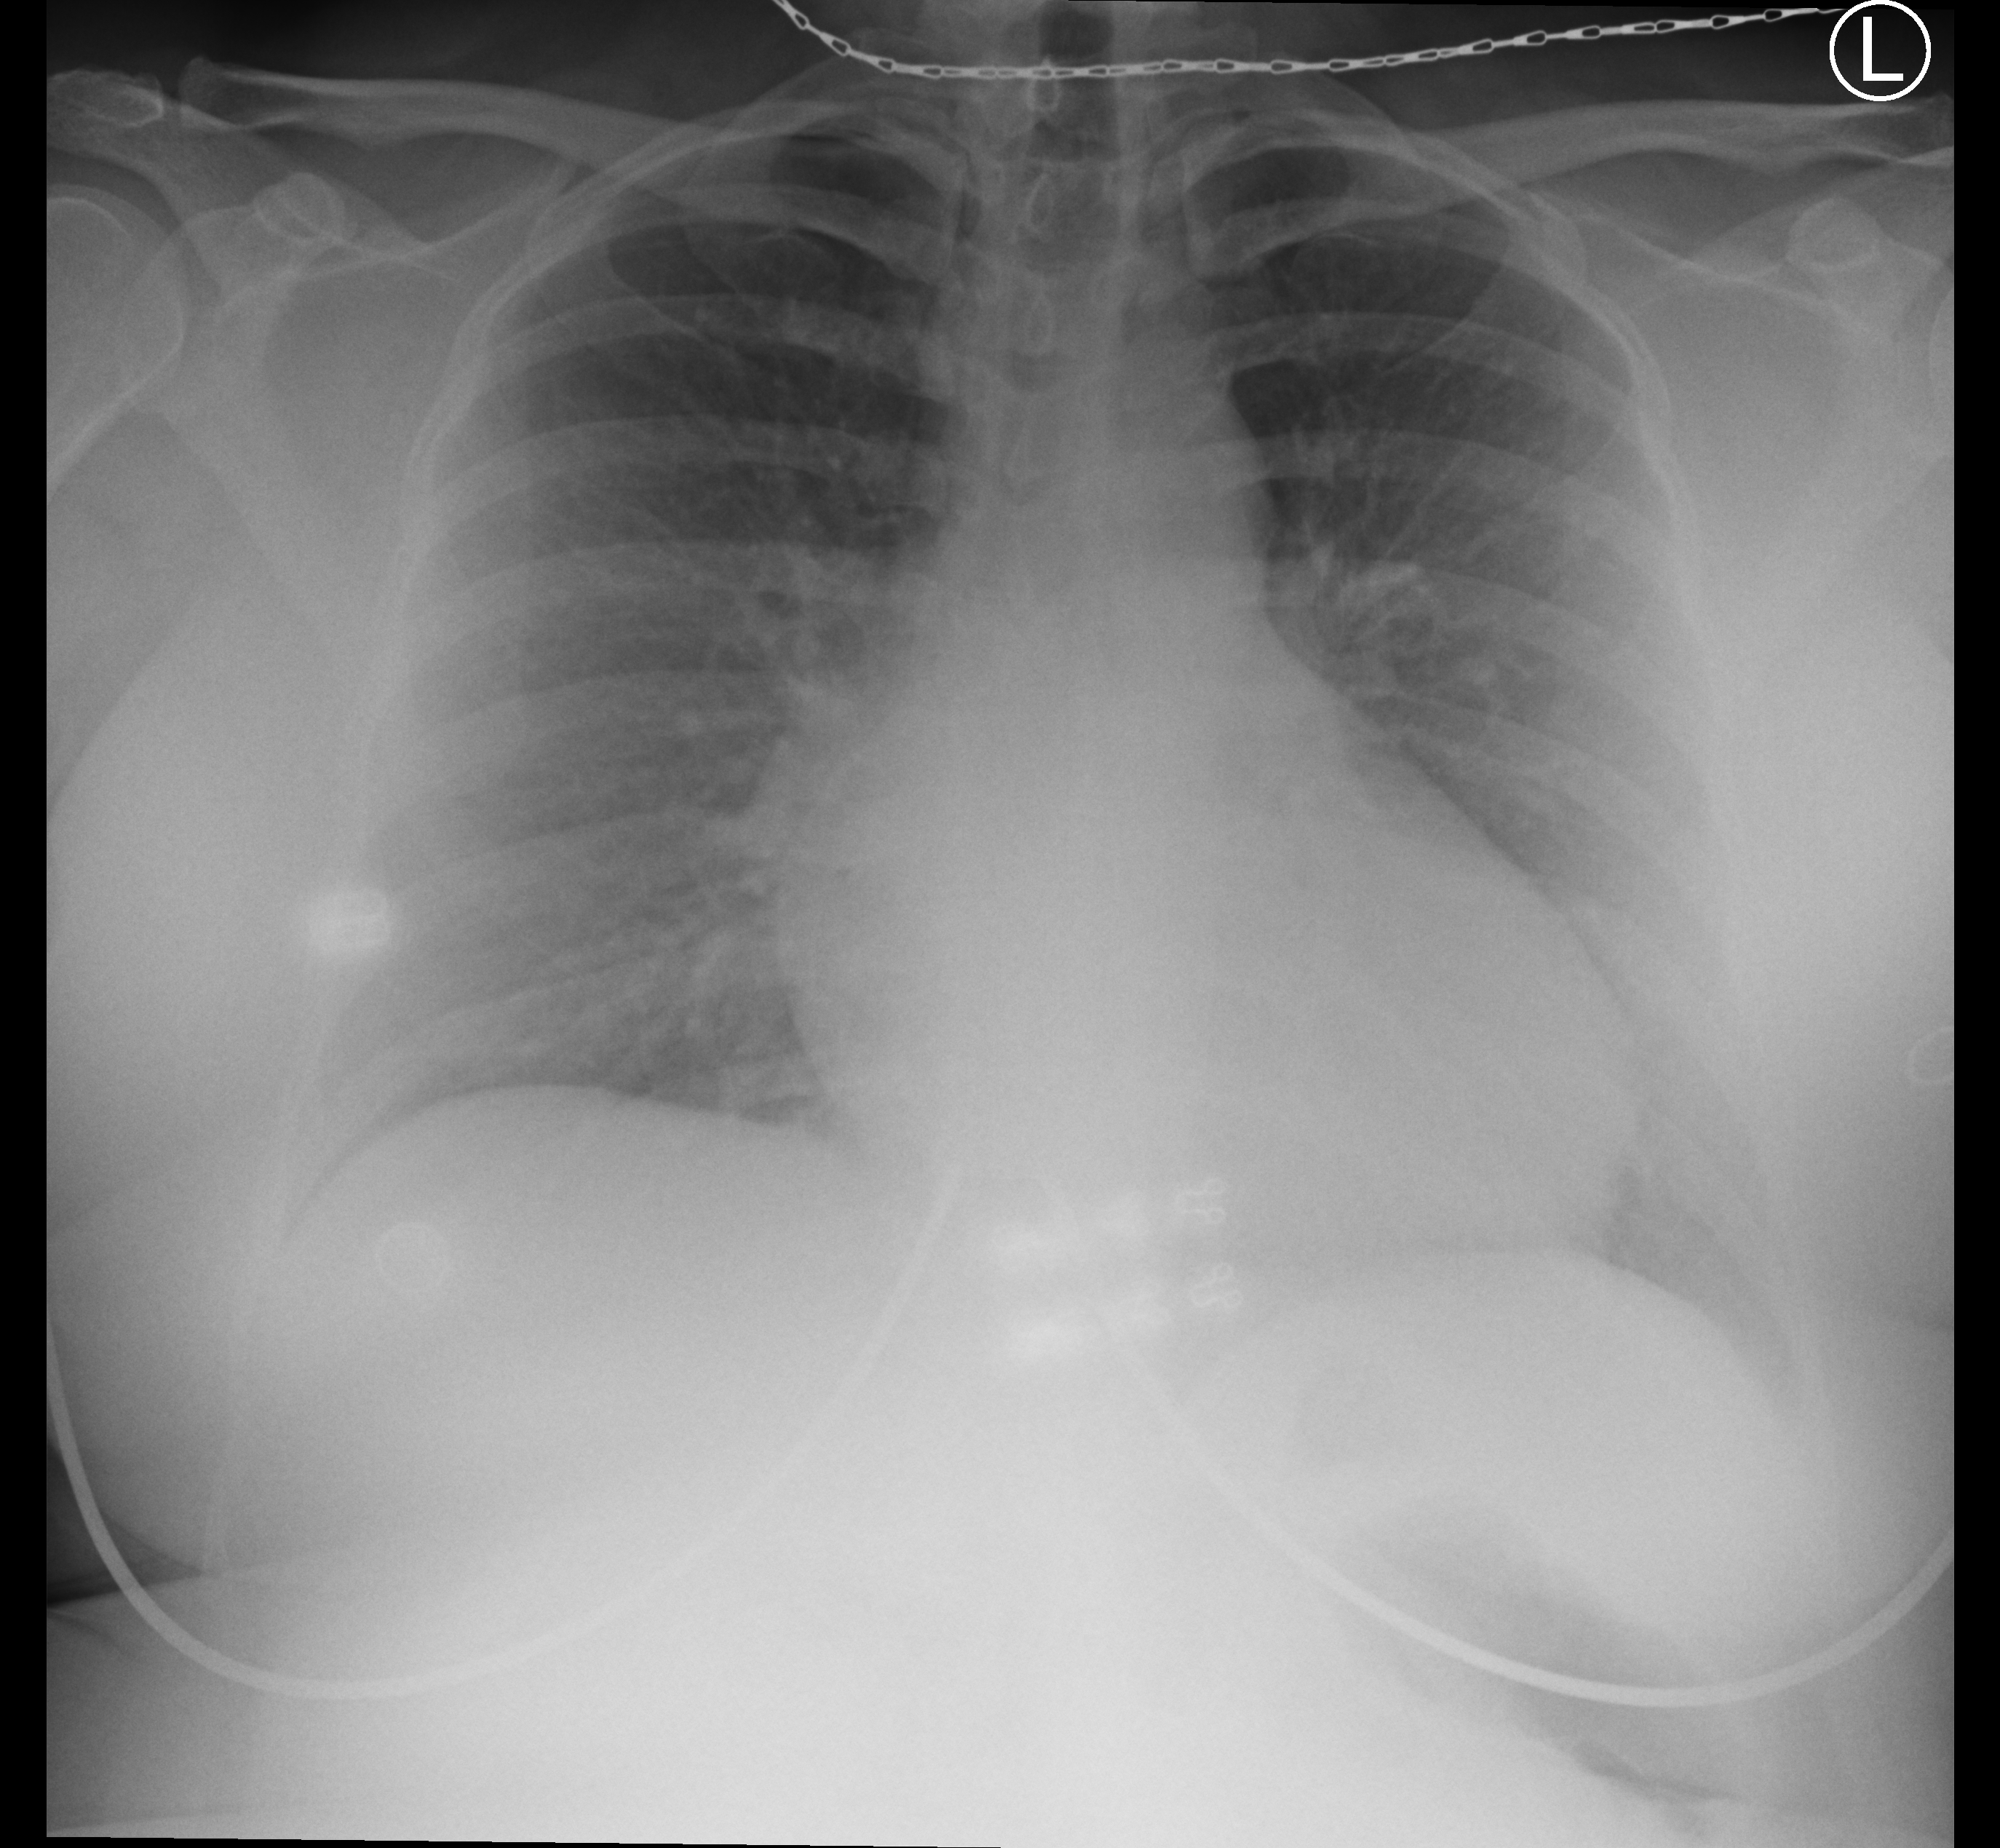
Chest X-ray (portable). Patient hospitalised with COVID-19; female, aged 18–59 years.
From the hospital-stay record, not from the radiograph (when in the stay this image was taken is not recorded): length of hospital stay: 1 day; hypertension (admission record): no; admitted to intensive care during this hospital stay: no.